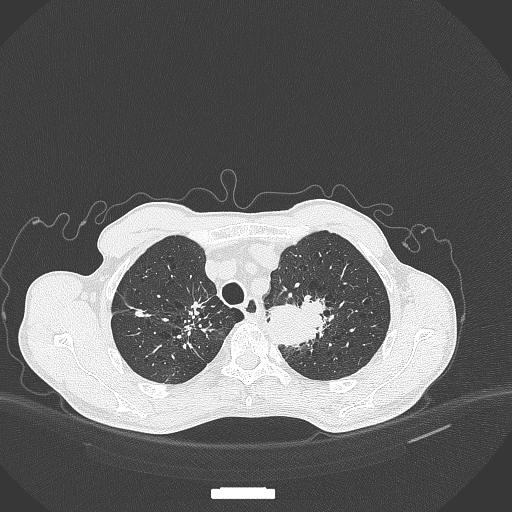
Chest CT, one axial slice. Reconstruction kernel B70f. 120 kVp. Lung window (W 1500 / L -600 HU). 1 mm slice thickness. 512 × 512 image matrix, field of view 400 × 400 mm. Patient: male, 65 years. Case-level facts recorded for this patient, not image findings: clinical TNM (as recorded): T2b N0 M0.
Outlined on this slice (rectangle marked by the reading radiologist):
- lung tumour (recorded histology: adenocarcinoma): bounding box [x1, y1, x2, y2] px = [262, 292, 336, 346]